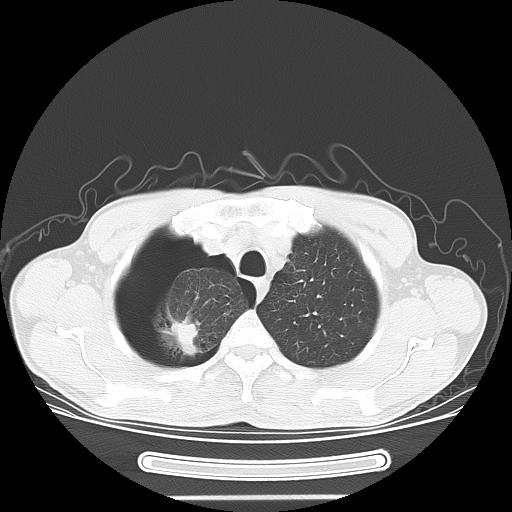
Chest CT, one axial slice; lung window (W 1500 / L -600 HU); 5 mm slice thickness; 512 × 512 image matrix, field of view 375 × 375 mm. Male patient. Case-level facts recorded for this patient, not image findings: clinical TNM (as recorded): T1c N0 M0.
Annotated regions visible in this slice (rectangle marked by the reading radiologist):
- lung tumour (recorded histology: adenocarcinoma): bounding box (x1, y1, x2, y2) in pixels: (163, 315, 199, 364)